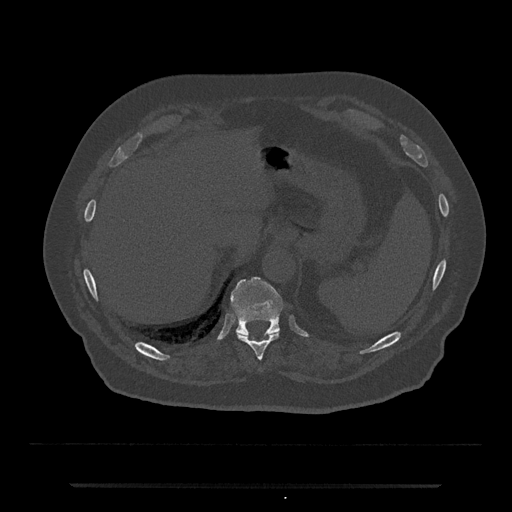
CT including the spine, one axial slice. Position 681 of 797 along the scan axis. 120 kVp. Bone window (W 1800 / L 400 HU). 0.5 mm slice thickness. 512 × 512 image matrix. Patient: male, 80 years. Case-level facts recorded for this patient, not image findings: primary cancer: prostate.
Annotated regions visible in this slice (semi-automatically segmented with operator editing):
- T10 vertebra: bounding box (x1, y1, x2, y2) in pixels: (237, 332, 279, 360)
- T11 vertebra: (231, 277, 284, 336)